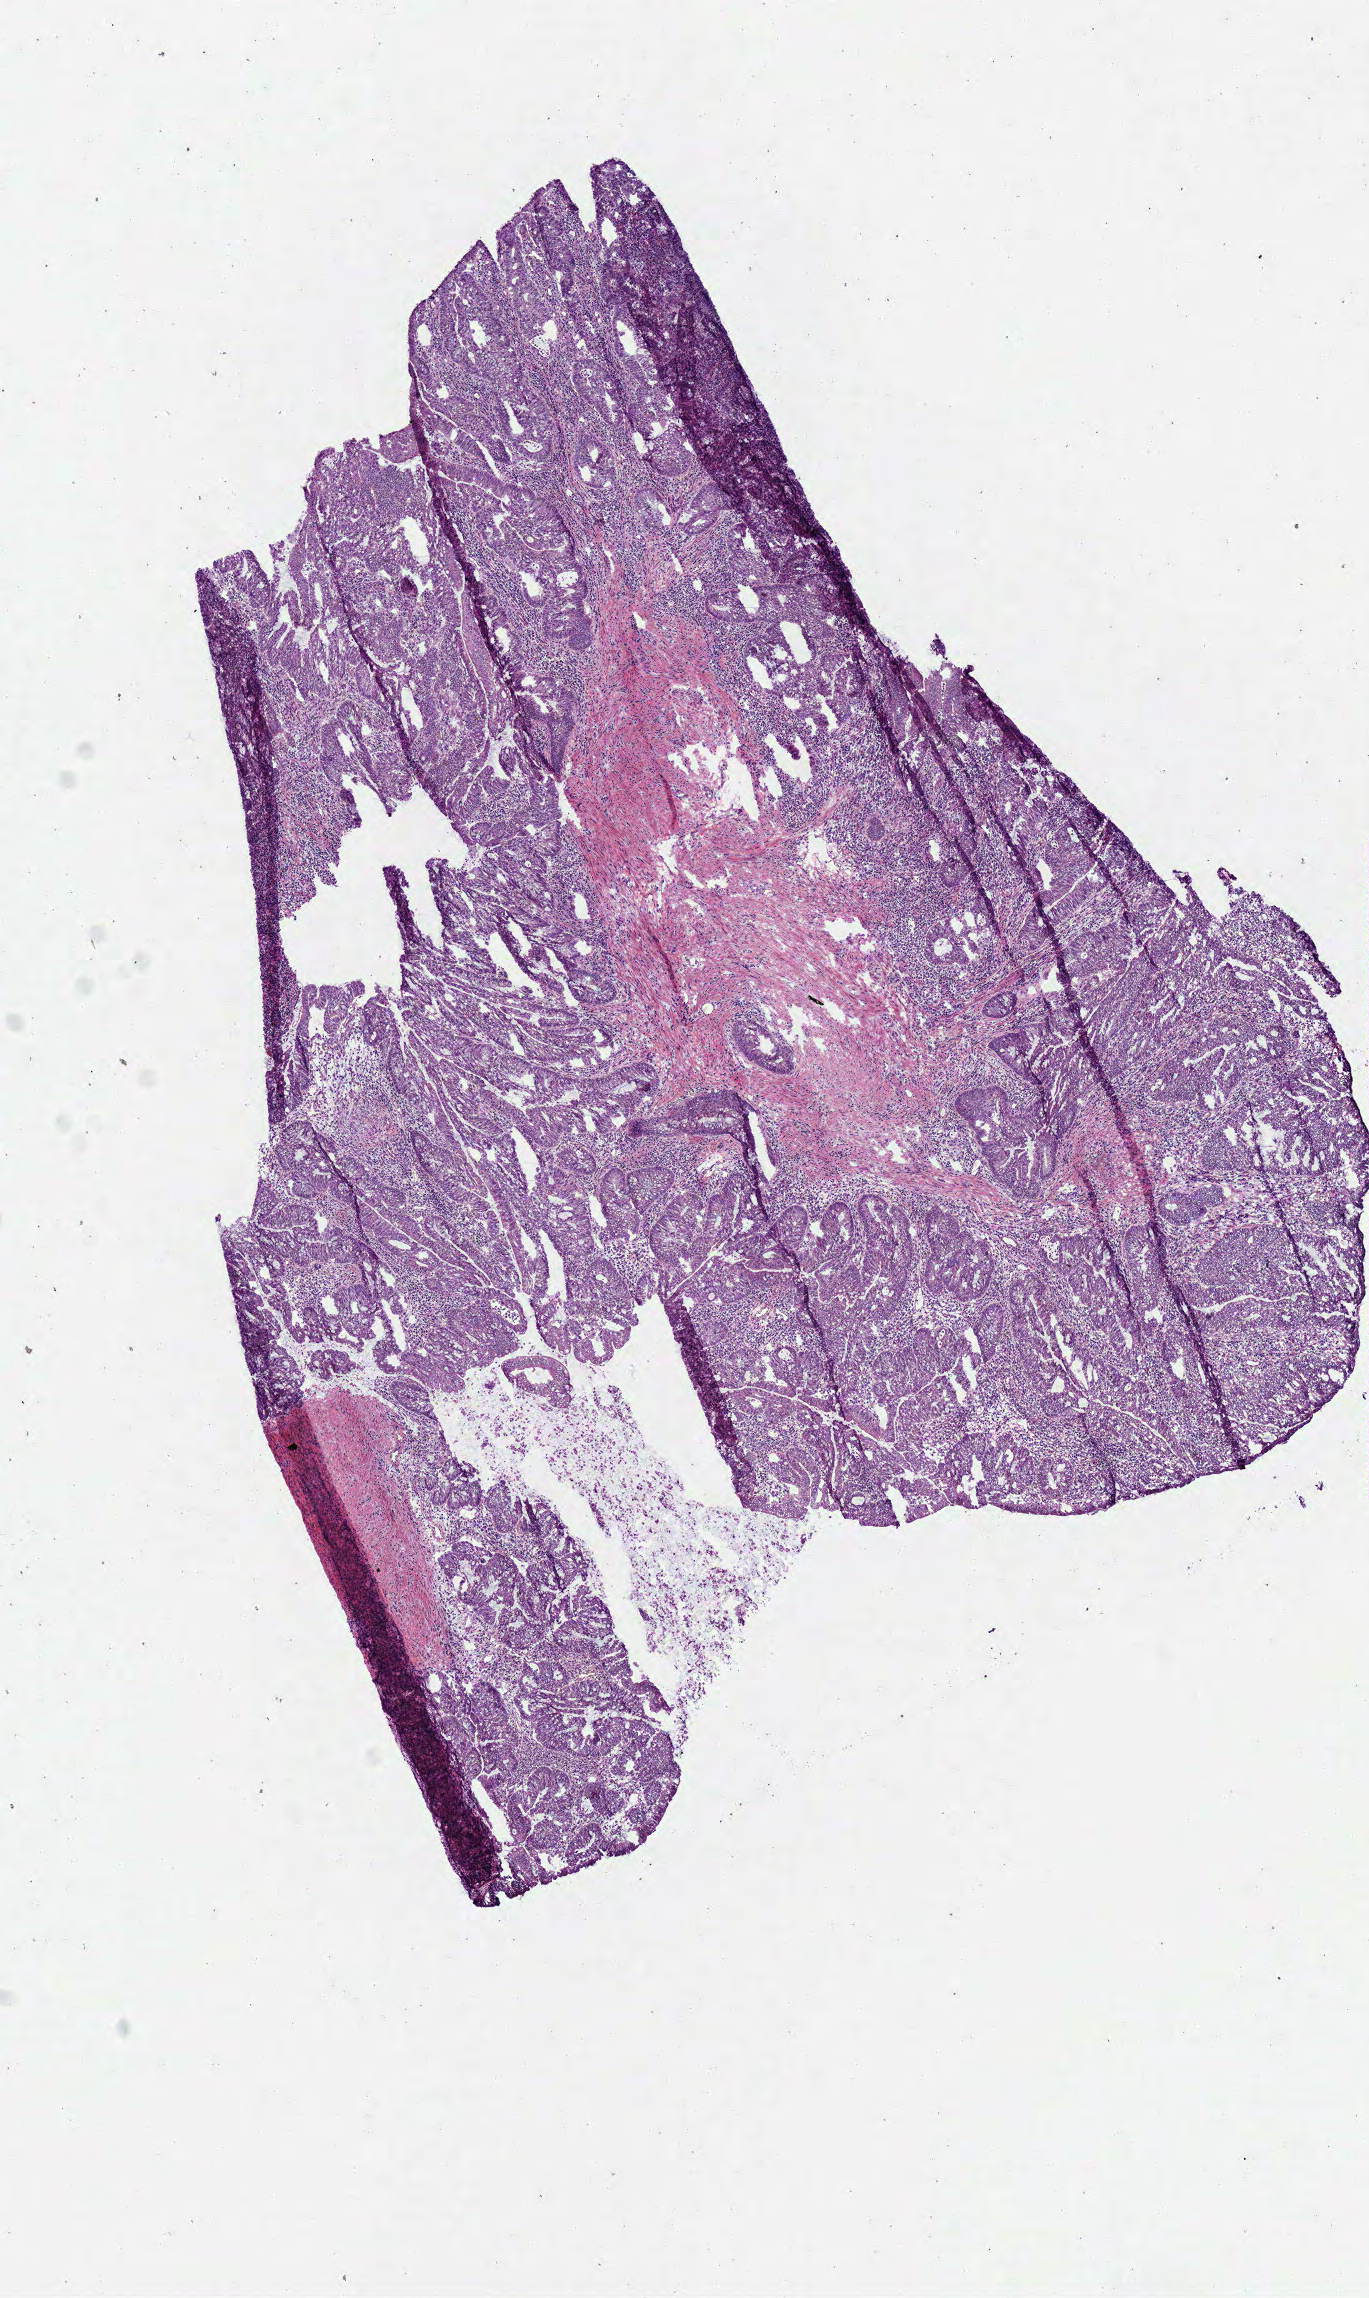
Whole-slide histology image, Hematoxylin and eosin (H&E) stained — whole scanned area (about 5.4 x 9.0 mm, slide scanned at 40x) shown as a low-resolution overview; frozen section; primary tumour sample from the colon. Patient: female, age at initial diagnosis 66 years. Slide review estimates, as recorded: tumour cells 75%, tumour nuclei 60%, normal cells 0%, stromal cells 25%, necrosis 0%.
Diagnosis: Adenocarcinoma, NOS (cecum). AJCC pathologic stage: IIIB.